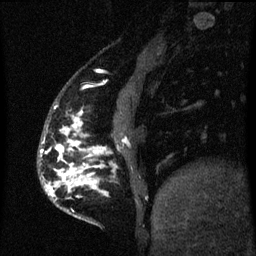
Breast MRI (dynamic contrast-enhanced), one sagittal slice. Dynamic contrast-enhanced series, image 2 of 3 at this slice position (ordered by acquisition). 1.5 T. TE 4.2 ms, TR 8 ms. 2 mm slice thickness. 256 × 256 image matrix, field of view 190 × 190 mm. Female patient, age 50 years.
Outlined on this slice (semi-automatic segmentation, software-assisted and operator-edited):
- analysis volume of interest (the breast-tissue region the enhancement analysis was run in; not a lesion): box from (x=46, y=111) to (x=101, y=223) px
- tumour enhancement mask (voxels above the 70 % enhancement threshold inside the analysis volume of interest): (x=46, y=111)–(x=100, y=196)